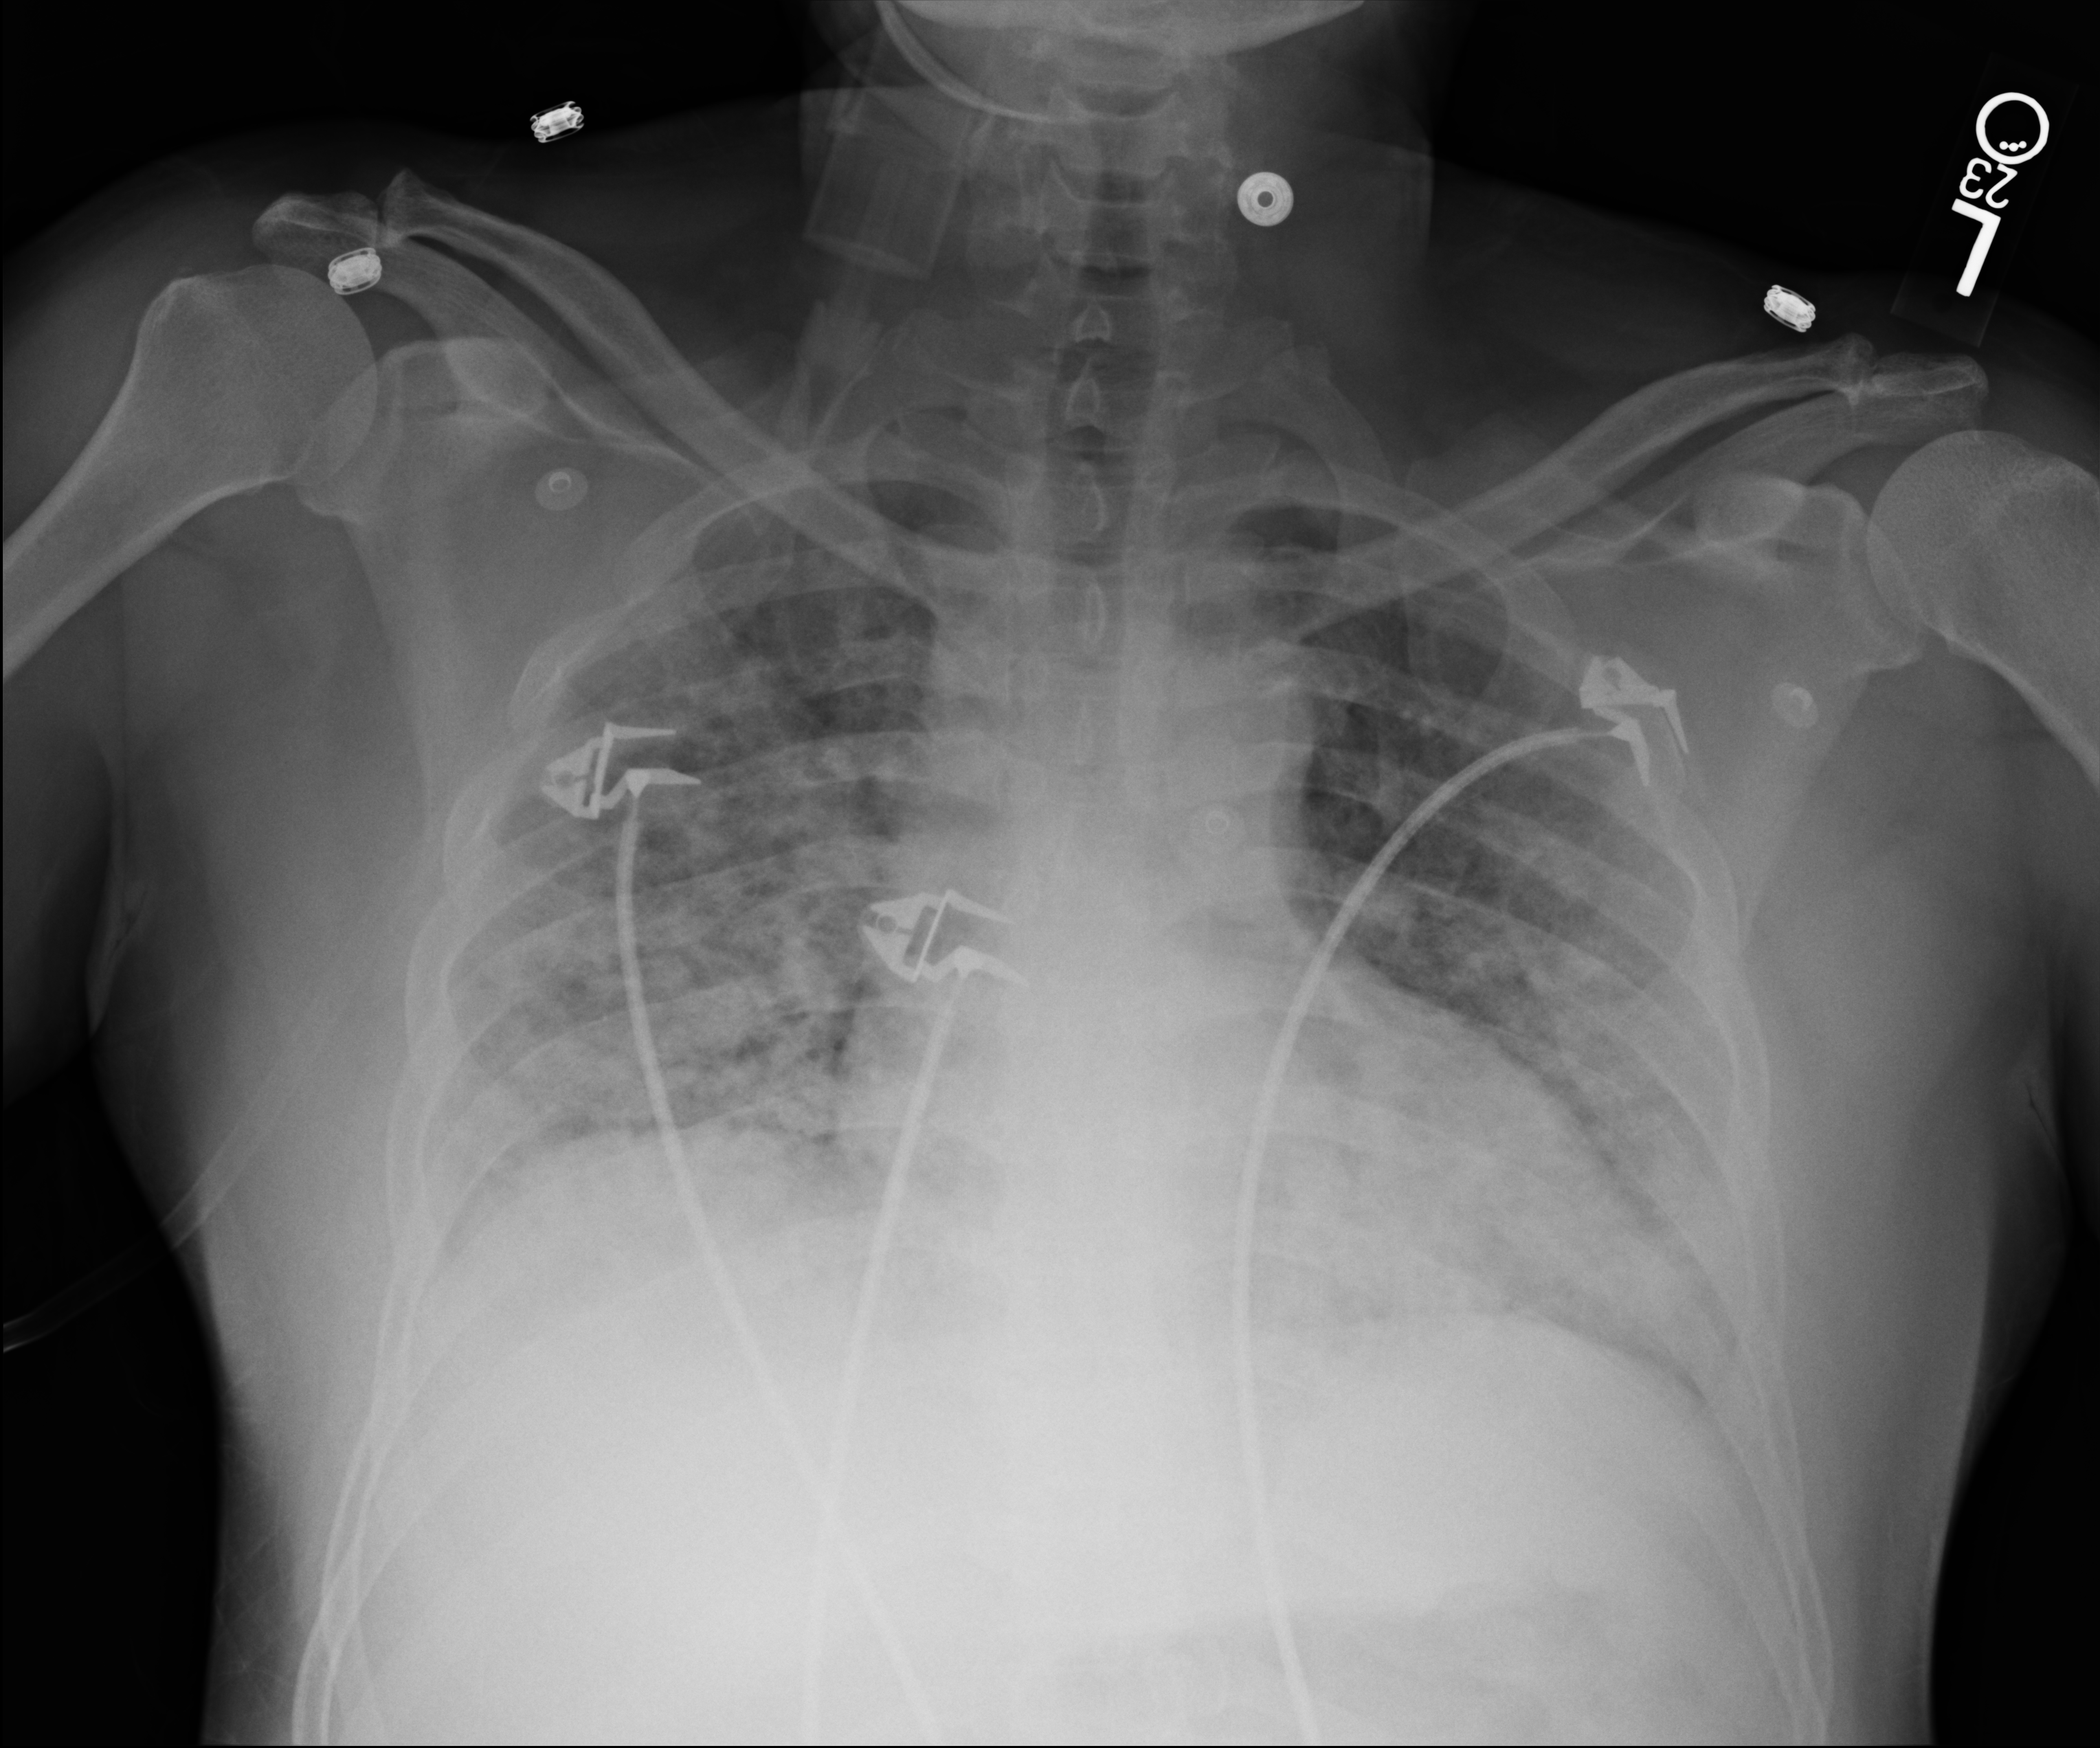
Chest X-ray (portable), anteroposterior (AP) projection. Male patient hospitalised with COVID-19, age 18–59 years.
Admission-level facts for this patient (not findings on this image; timing relative to this image not recorded): mechanically ventilated during this hospital stay: no; other chronic lung disease (admission record): no.